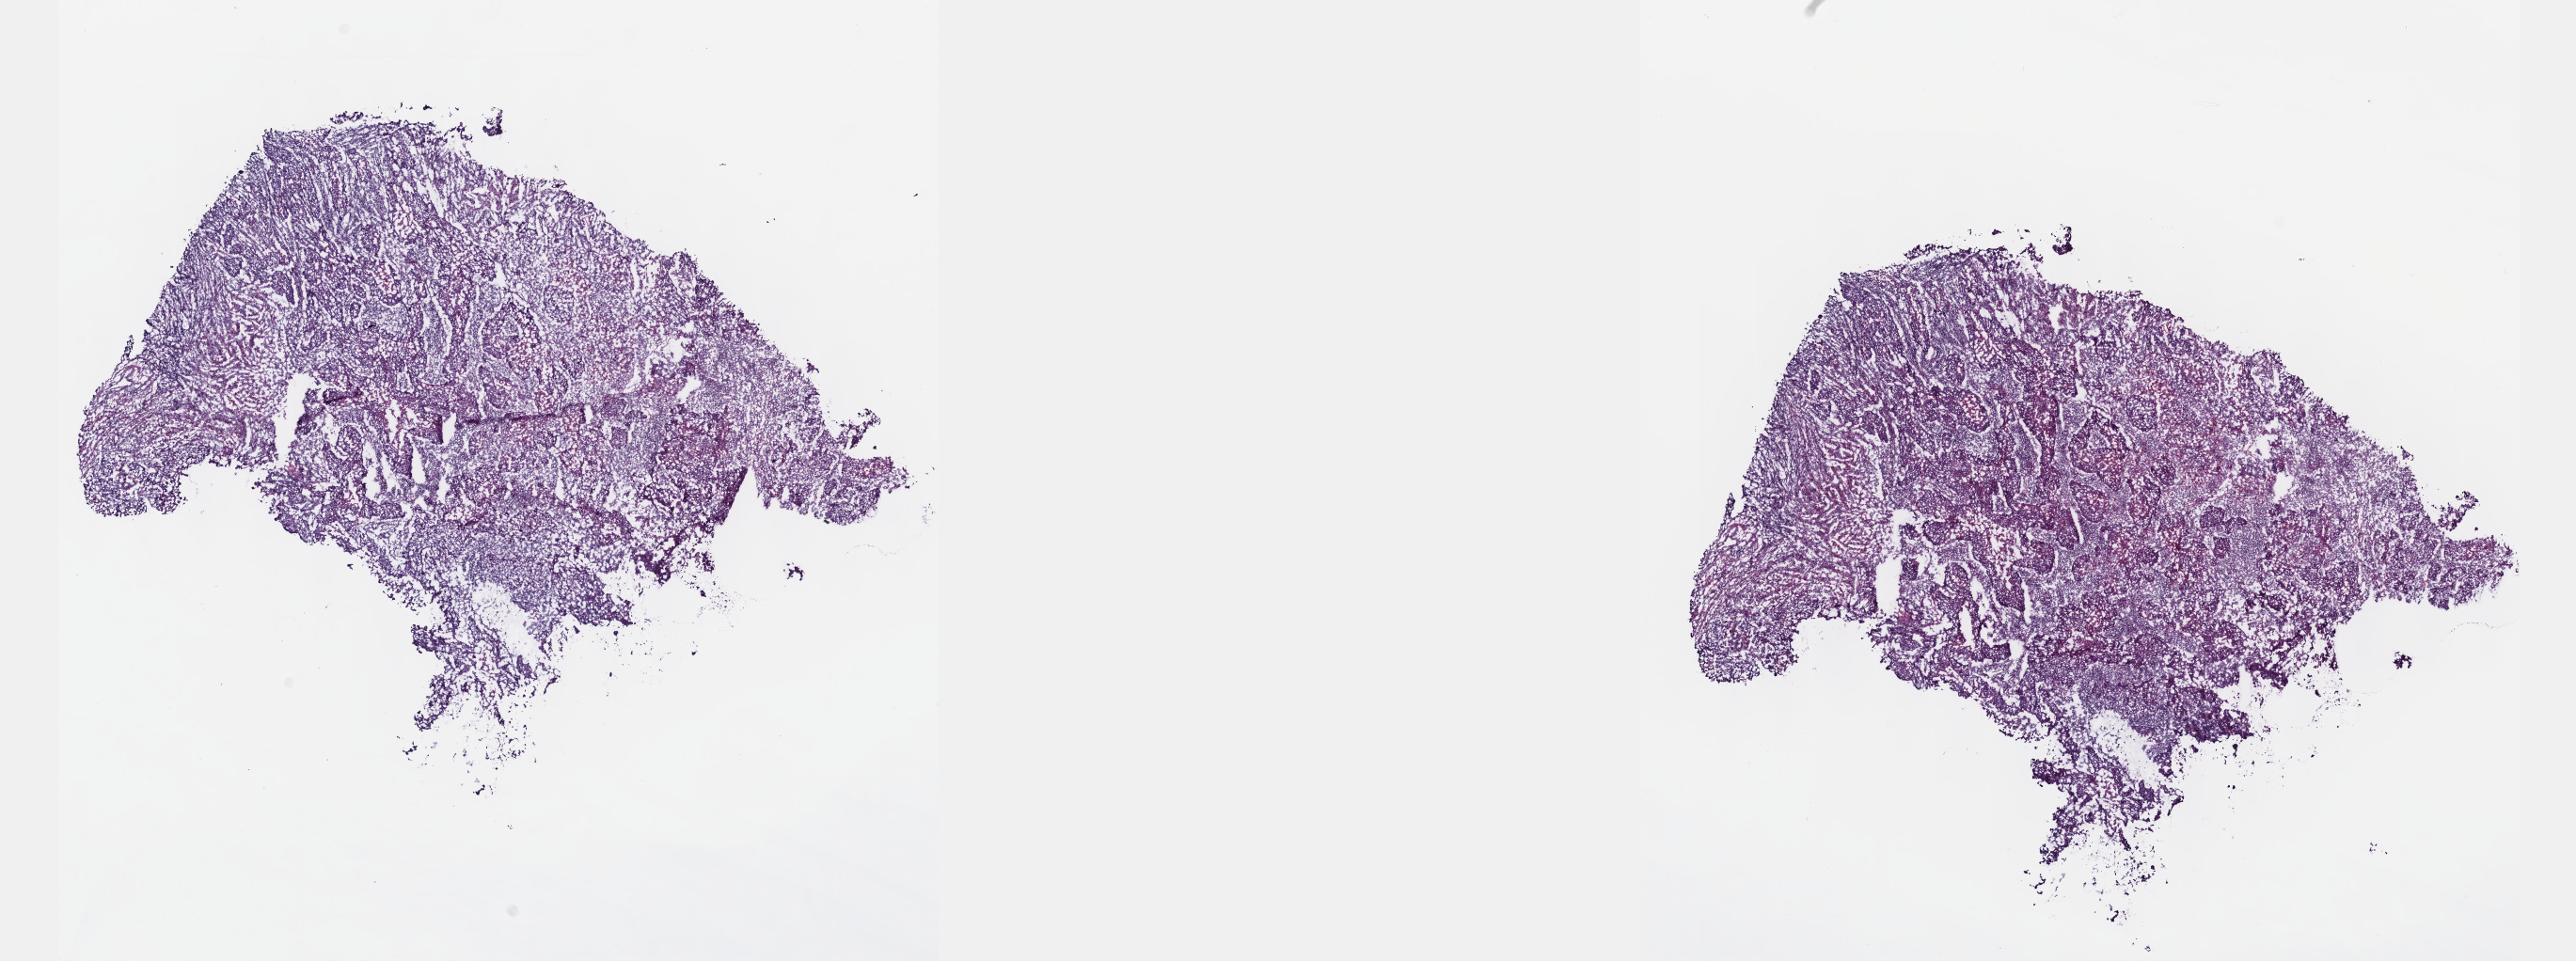
Whole-slide histology image, Hematoxylin and eosin (H&E) stained — whole scanned area (about 22.1 x 8.3 mm, from a 40x scan) shown as a low-resolution overview; frozen section; sample: primary tumour, lung. Patient: female, age at initial diagnosis 57 years. Pathologist review of this section (percent, as recorded): tumour cells 70%, tumour nuclei 80%, normal cells 0%, stromal cells 30%, necrosis 0%. Infiltration values recorded for this section: lymphocyte infiltration 0%, monocyte infiltration 0%, neutrophil infiltration 0%.
AJCC pathologic stage: IA (5th edition). Laterality: right. Diagnosis: Squamous cell carcinoma, NOS.